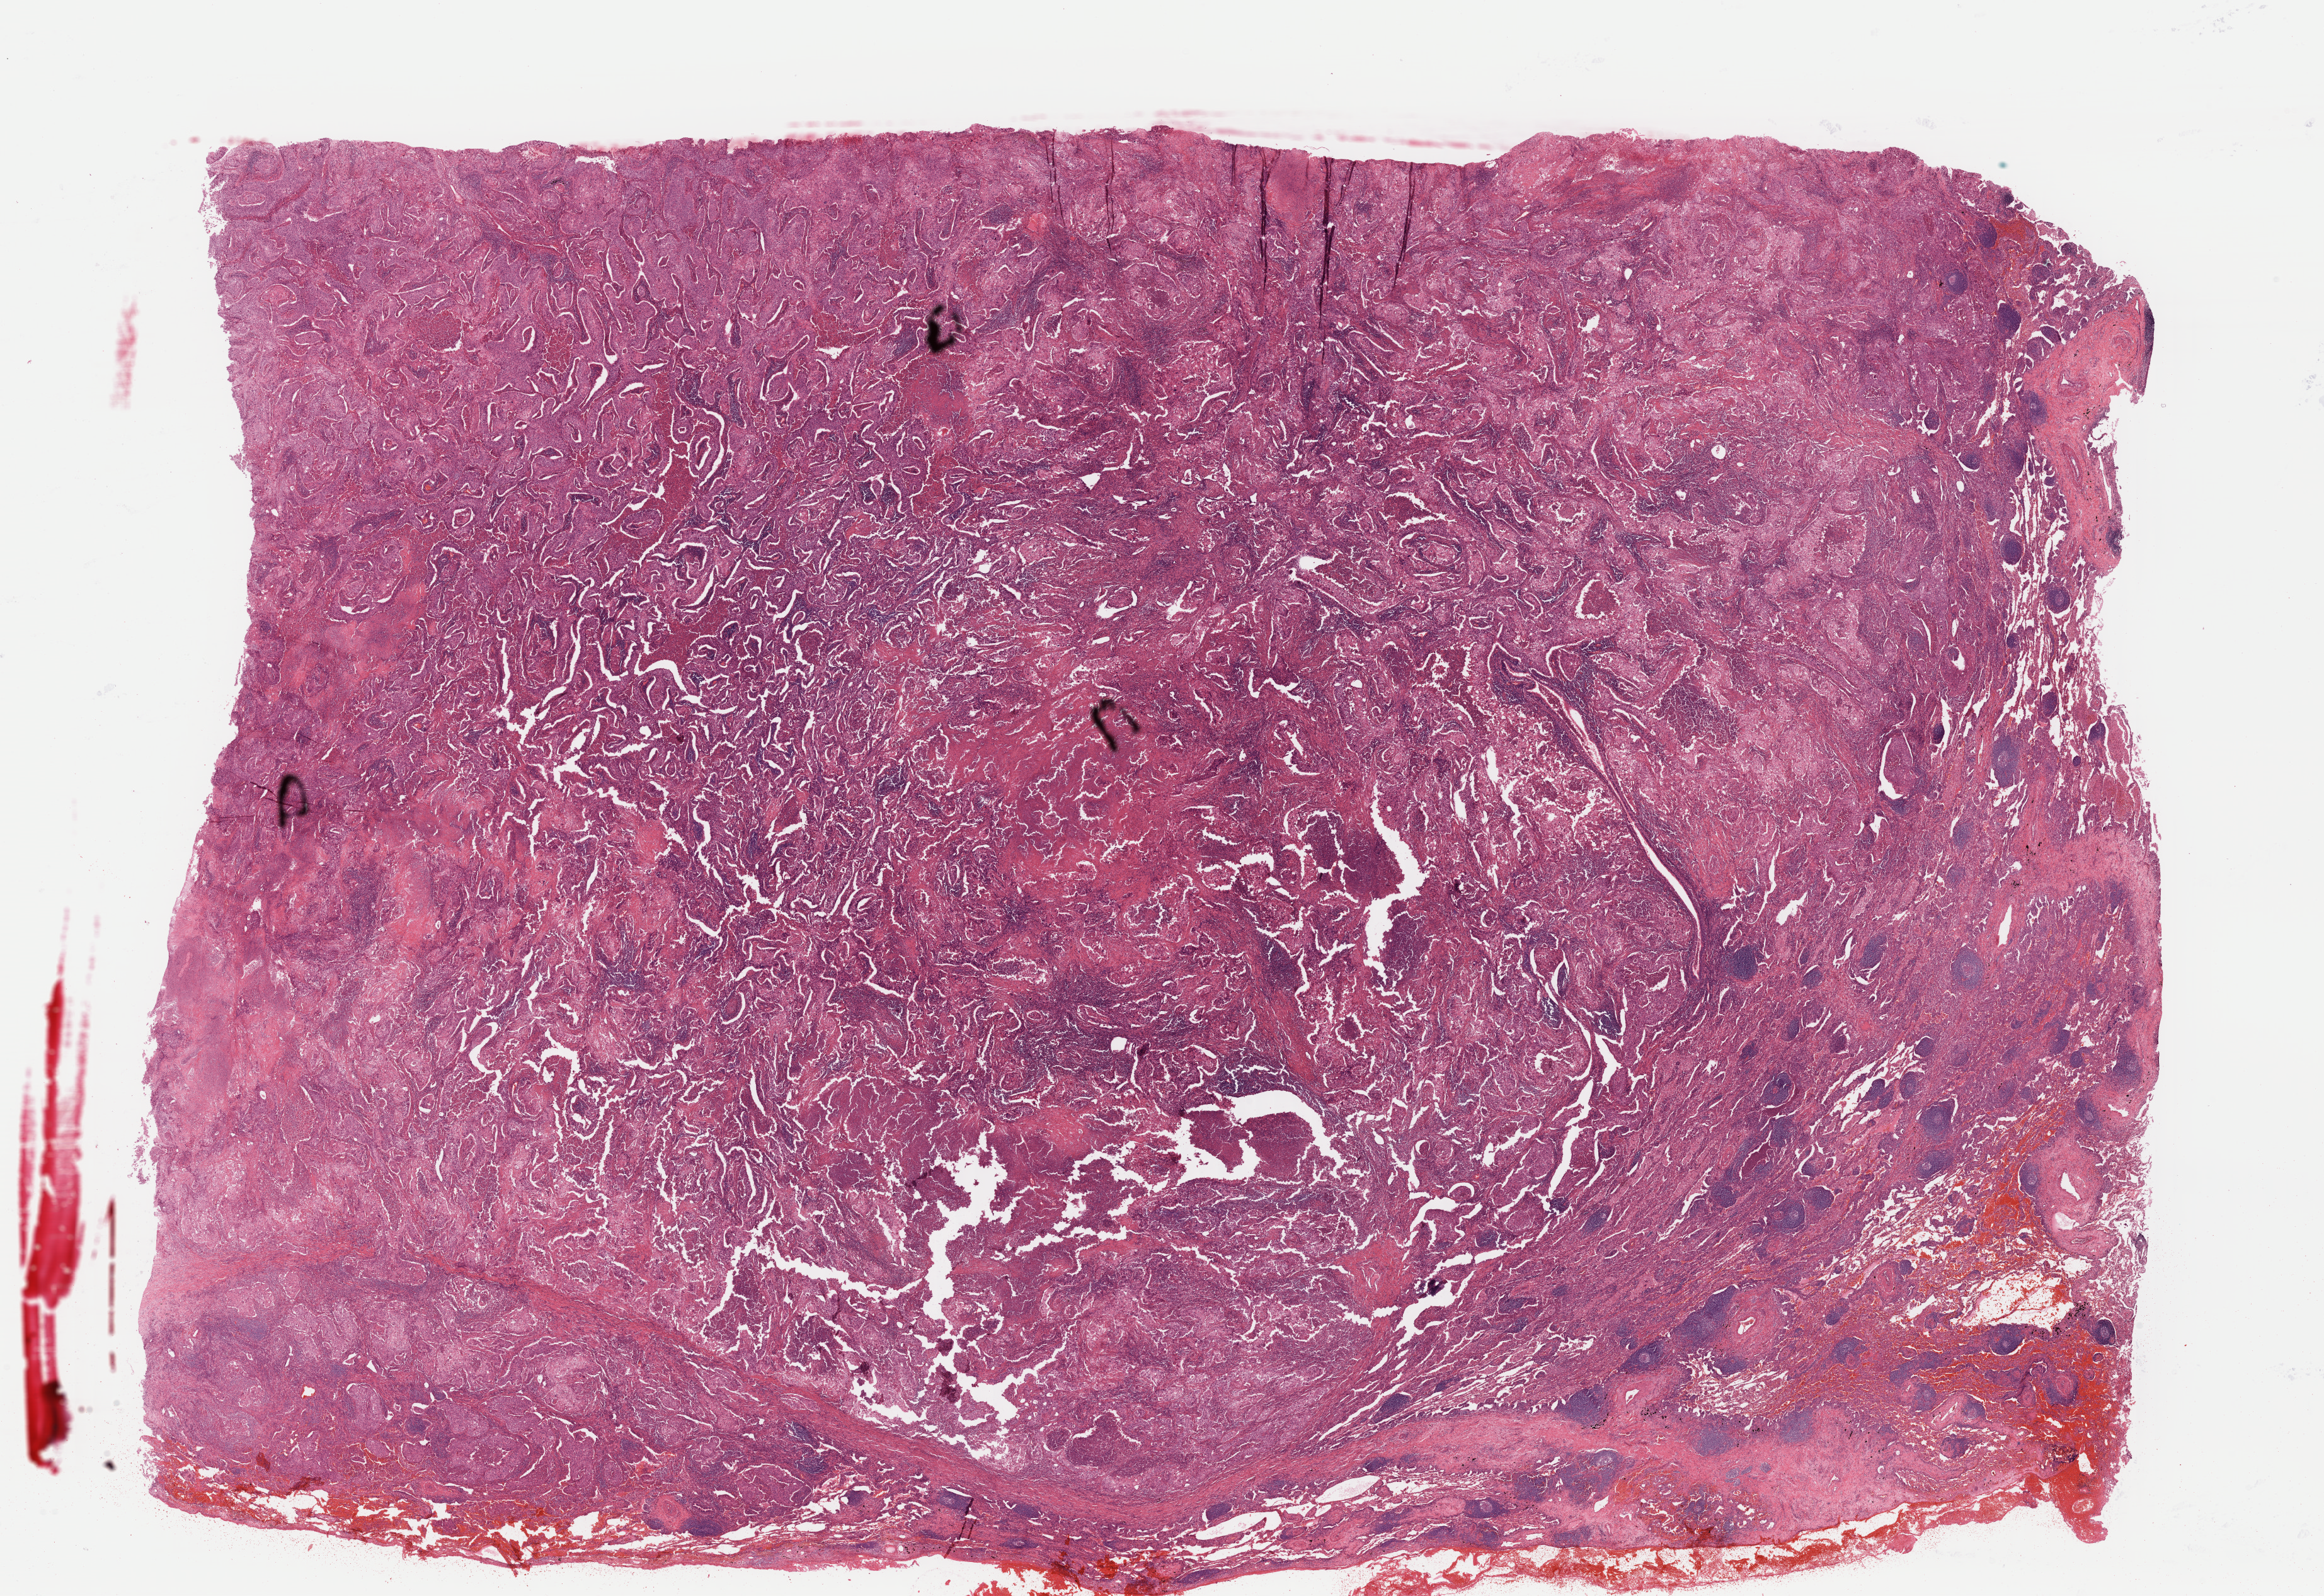
Whole-slide histology image, H&E, a low-resolution overview of the entire scanned area, about 29.1 x 20.0 mm (from a 40x scan). Formalin-fixed paraffin-embedded (FFPE) diagnostic section. Sample: primary tumour, lung. Male, age 63 years at initial diagnosis.
Diagnosis: Squamous cell carcinoma, NOS (middle lobe, lung). AJCC pathologic stage: IIA (7th edition).